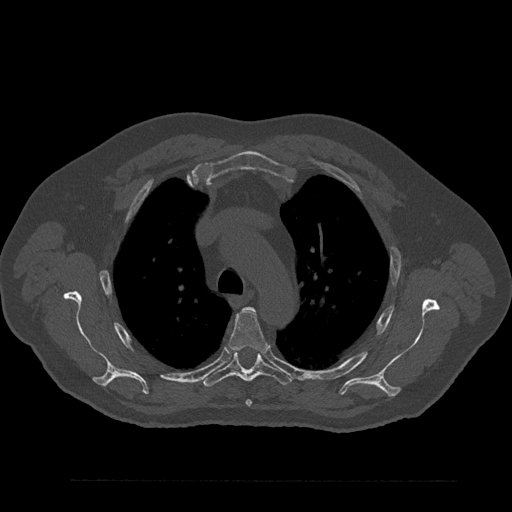
CT including the spine, one axial slice; position 623 of 797 along the scan axis; 120 kVp; bone window (W 1800 / L 400 HU); 0.5 mm slice thickness; 512 × 512 image matrix. Patient: male, 61 years. Case-level facts recorded for this patient, not image findings: primary cancer: prostate.
Structures marked on this image (semi-automatically segmented with operator editing):
- T4 vertebra: bounding box <228,307,267,407> (left, top, right, bottom; pixels)
- T5 vertebra: <202,351,291,387>